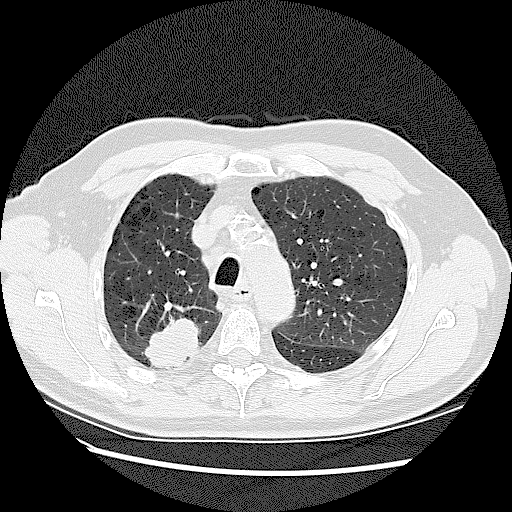
Low-dose screening chest CT, one axial slice; position 94 of 128 along the scan axis; reconstruction kernel LUNG; 120 kVp; lung window (W 1500 / L -600 HU); 512 × 512 image matrix.
Outlined on this slice (outlined manually by an expert reader):
- lesion 2 (tumor, upper lobe of right lung): bounding box [x1, y1, x2, y2] px = [144, 317, 198, 368]